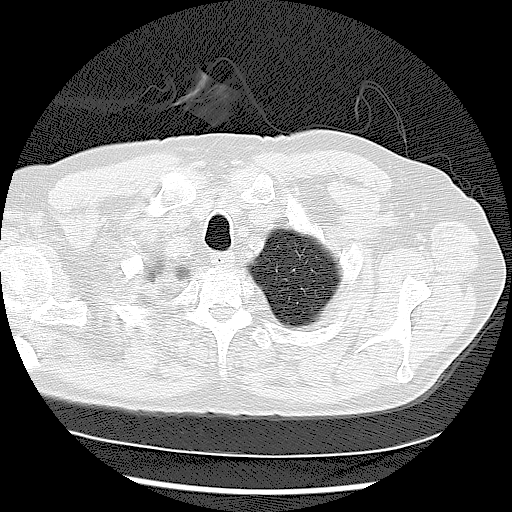
Low-dose screening chest CT, one axial slice; slice 107 of 122 in the series (ordered by position); 120 kVp; lung window (W 1500 / L -600 HU); 2.5 mm slice thickness; 512 × 512 image matrix, field of view 360 × 360 mm.
Outlined on this slice (outlined manually by an expert reader):
- lesion 2 (tumor, upper lobe of right lung): bounding box [x1, y1, x2, y2] px = [150, 270, 182, 300]